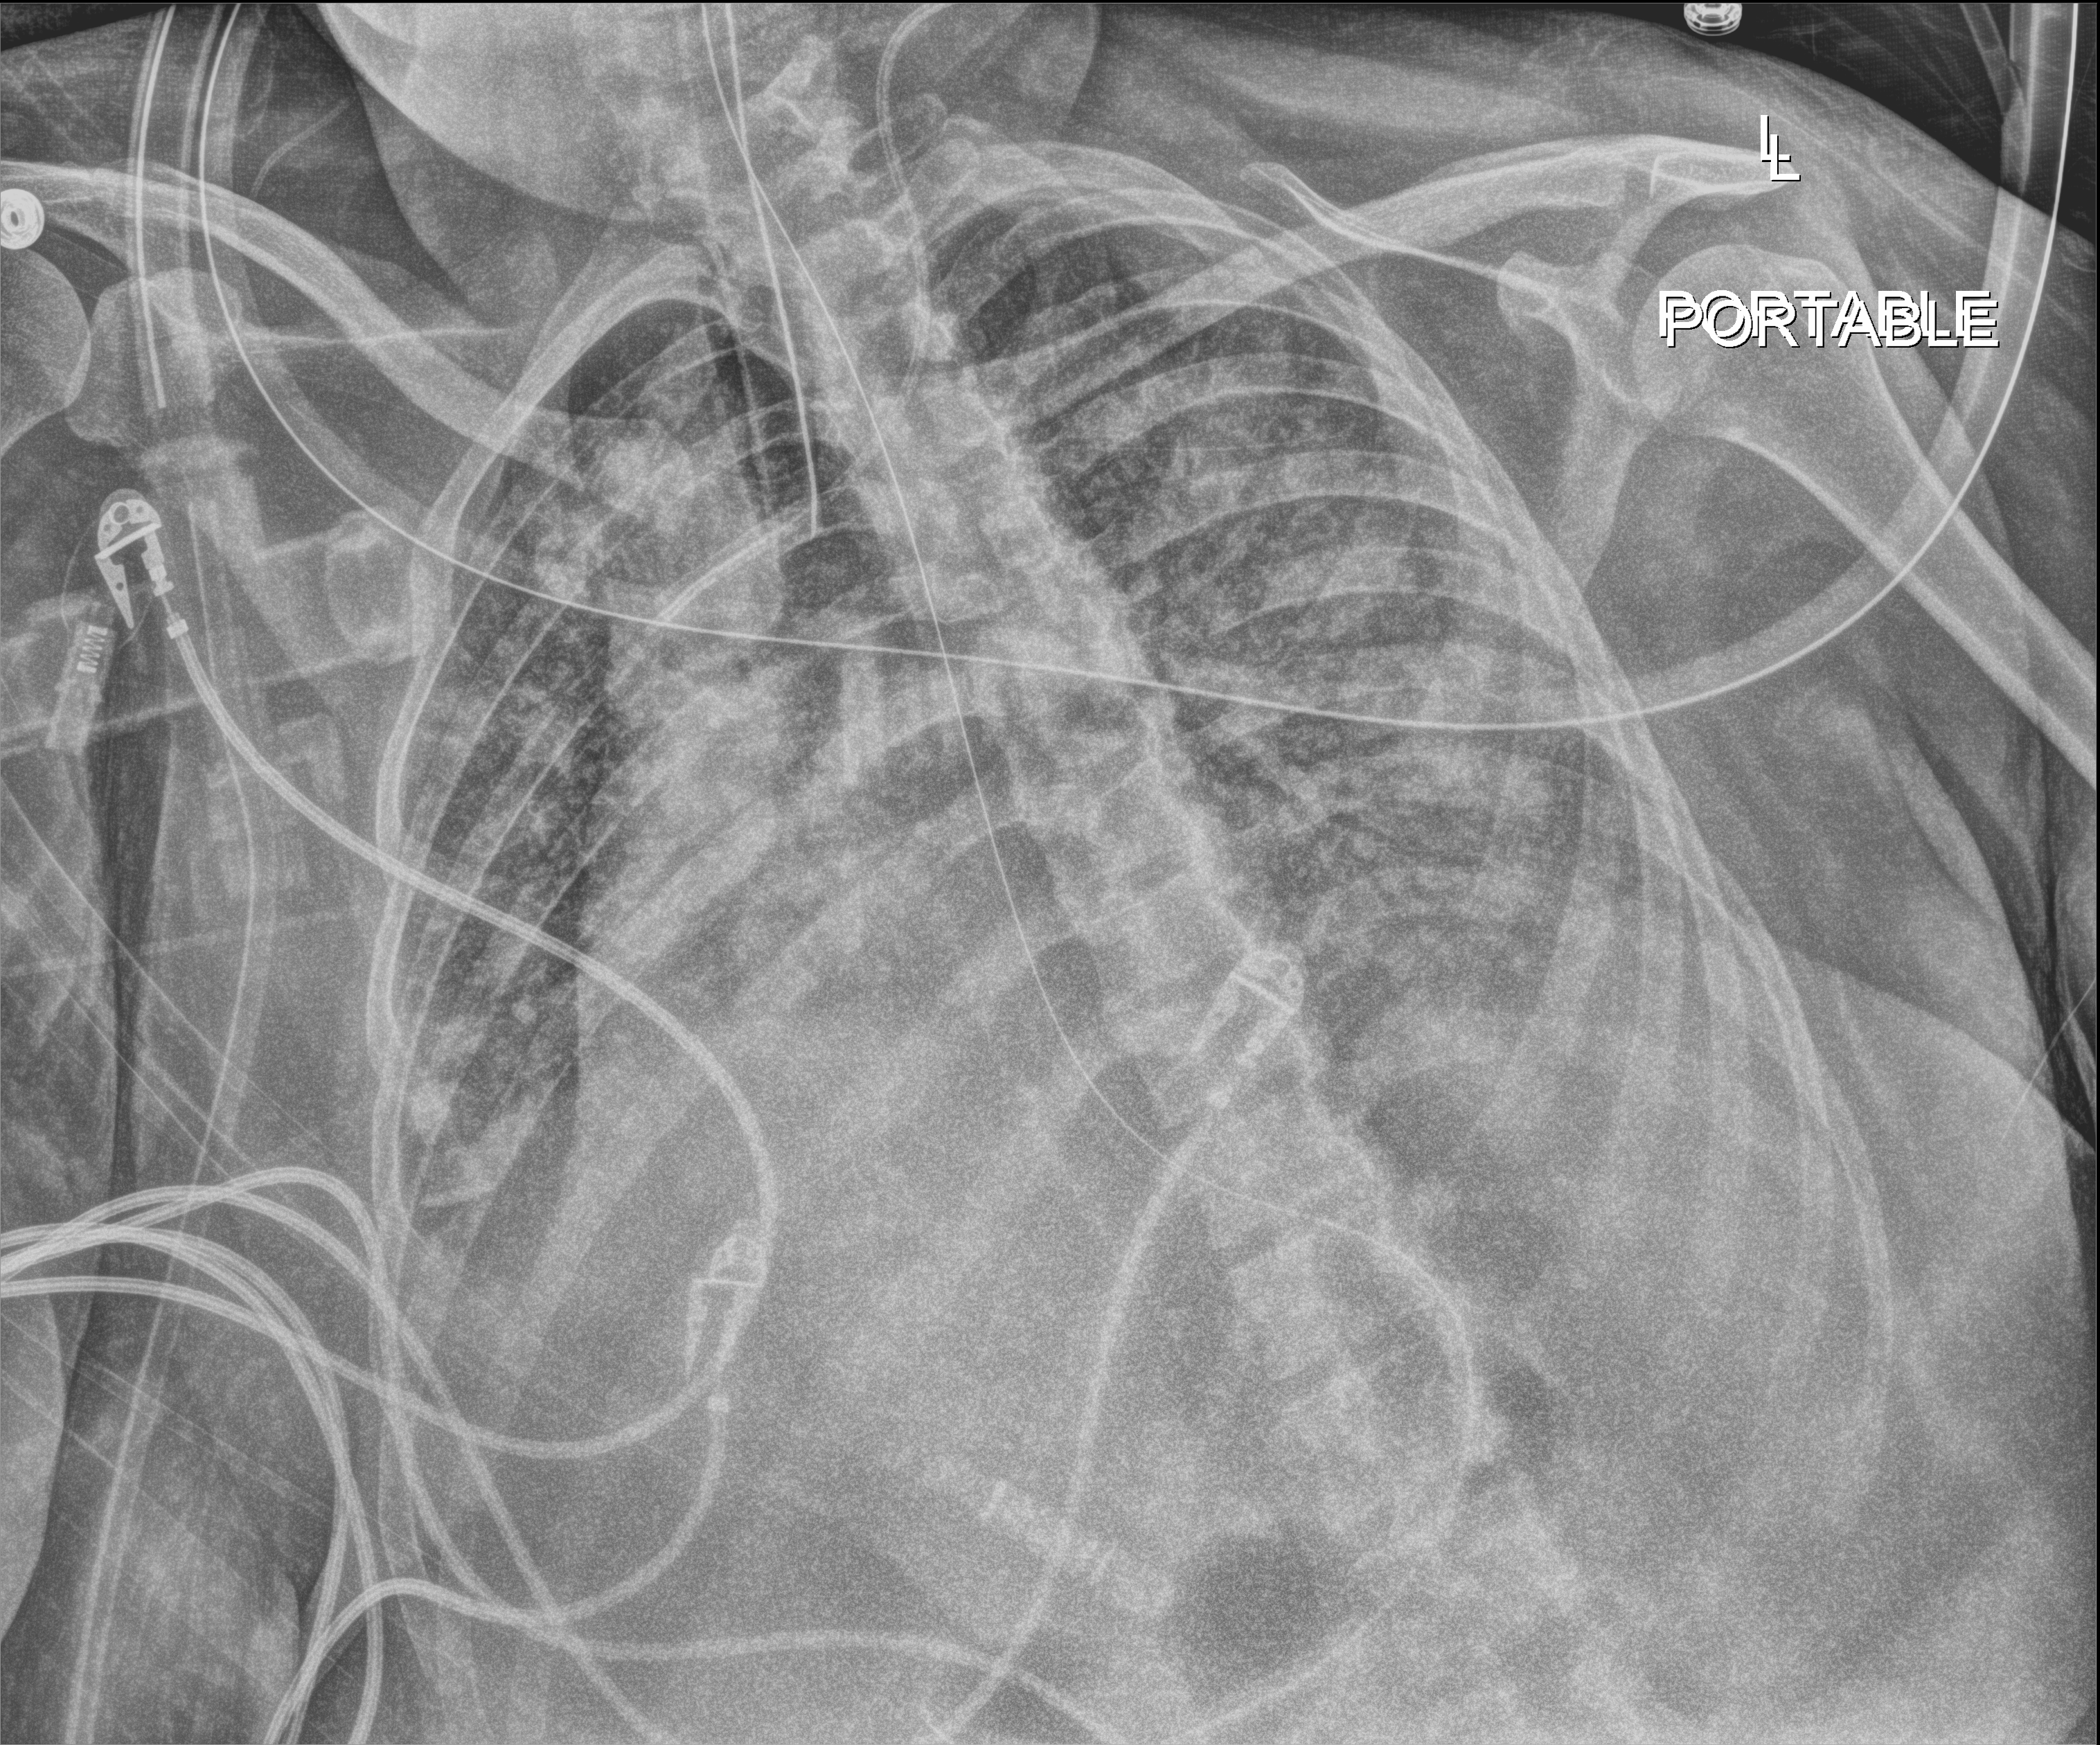
Chest radiograph, anteroposterior (AP) projection. Patient hospitalised with COVID-19; female, aged 18–59 years.
Admission-level facts for this patient (not findings on this image; timing relative to this image not recorded): mechanically ventilated during this hospital stay: yes.